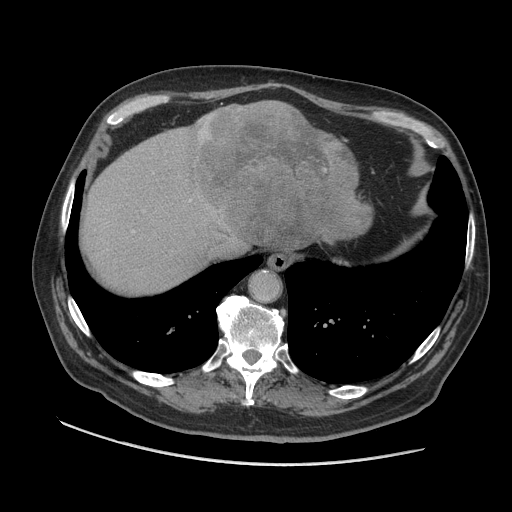
Contrast-enhanced abdominal CT (liver protocol), one axial slice. Slice 82 of 109 in the series (ordered by position). 140 kVp. Soft-tissue window (W 400 / L 40 HU). 512 × 512 image matrix, field of view 420 × 420 mm. From the clinical record (not read from this slice): diagnosis: hepatocellular carcinoma (patient treated with transarterial chemoembolisation; whether this scan precedes or follows treatment is not stated here); TNM stage (as recorded): Stage-I; Child-Pugh class: A; tumour nodularity: uninodular.
Outlined on this slice (semi-automatically segmented with operator editing):
- liver parenchyma outside the tumour (the mass and vessels are separate outlines, so this box may not span the whole liver): bounding box [x1, y1, x2, y2] px = [82, 100, 358, 292]
- mass: [190, 101, 372, 248]